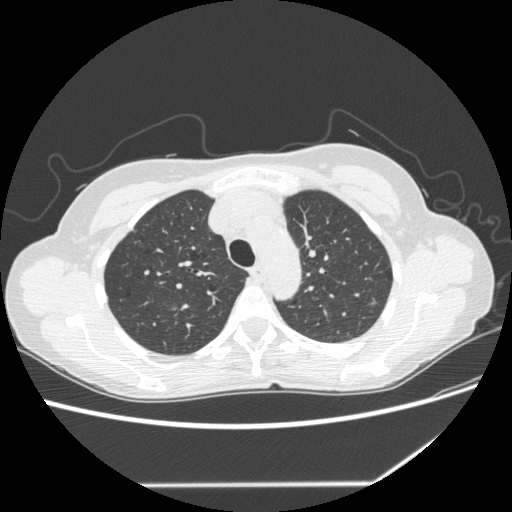
Axial slice from a low-dose chest CT screening exam, second annual screen, lung window (W 1500 / L -600 HU), 1.25 mm slice thickness. Female participant, aged 61 years at enrolment. Former smoker at enrolment.
Lesion marked by an expert reader, bounding box <357,292,386,319> (left, top, right, bottom; pixels). Screening reader's record for this exam (one nodule recorded; not confirmed to be the boxed lesion): non-calcified nodule or mass ≥4 mm, left upper lobe, 8 × 7 mm, poorly defined margins, mixed attenuation, pre-existing on the prior screen: yes; interval growth: yes.